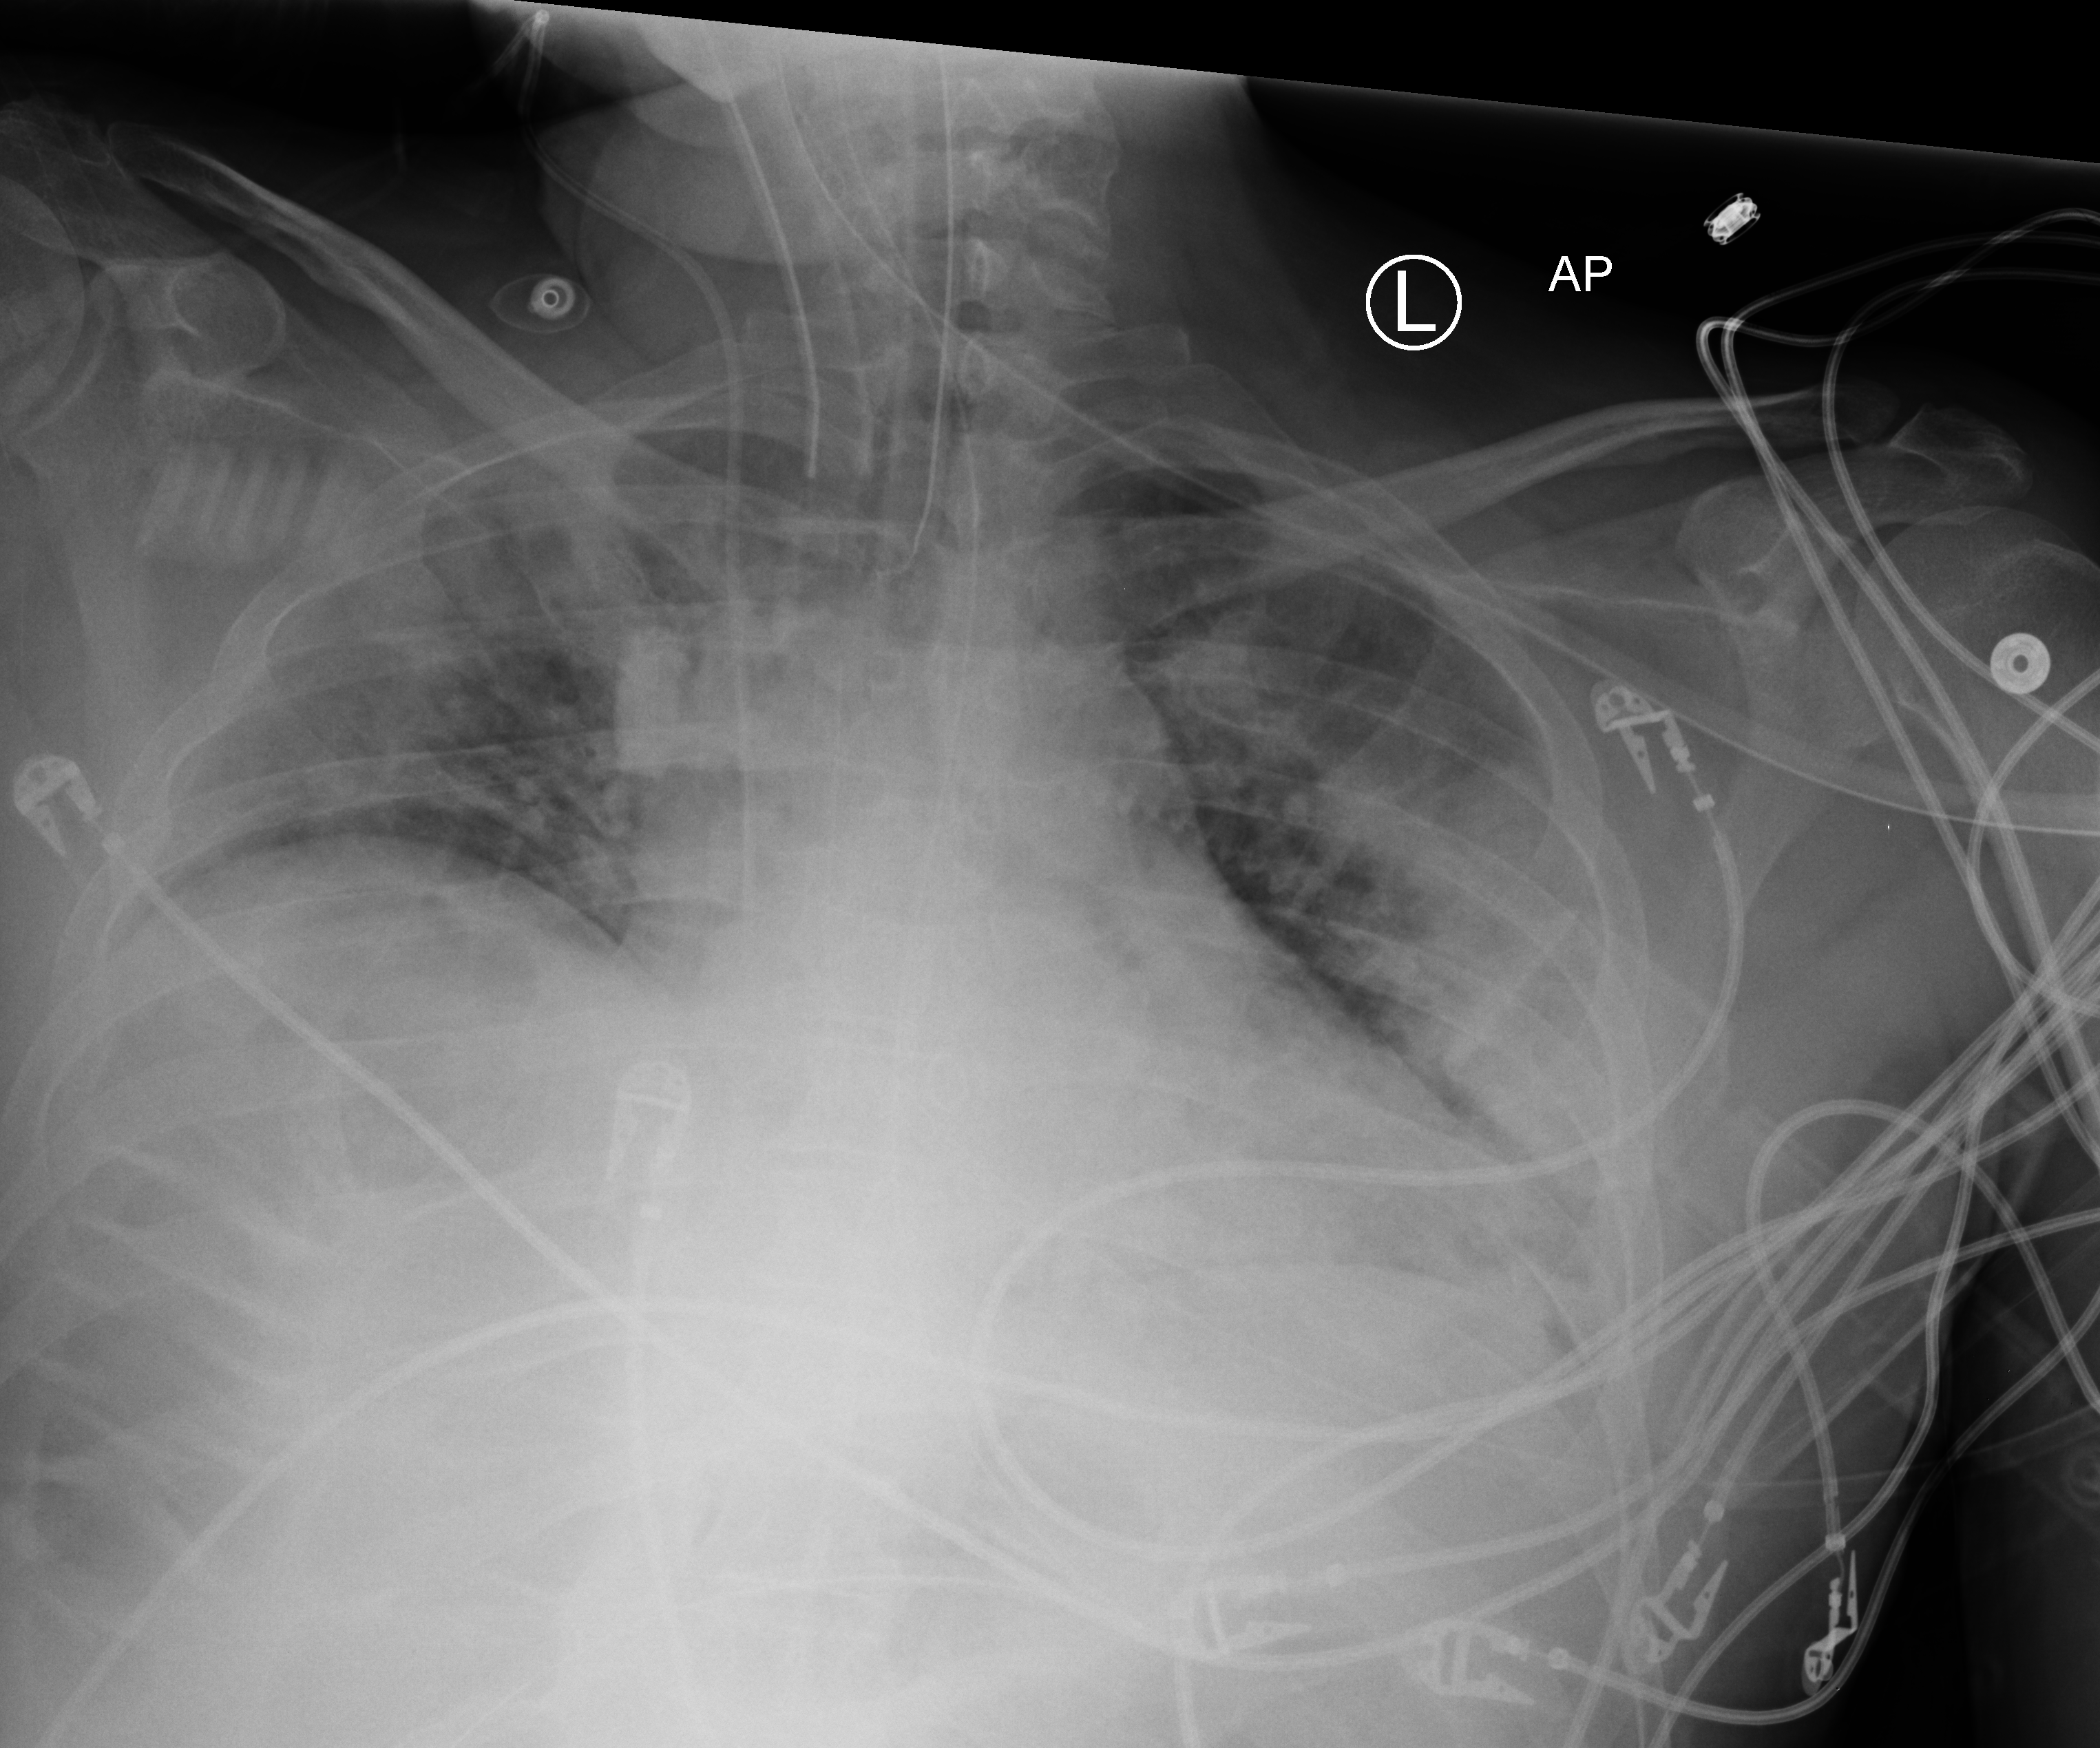
Chest X-ray (portable), anteroposterior (AP) projection. Patient hospitalised with COVID-19; male, aged 18–59 years.
From the hospital-stay record, not from the radiograph (when in the stay this image was taken is not recorded): mechanically ventilated during this hospital stay: yes; other chronic lung disease (admission record): no; admitted to intensive care during this hospital stay: yes.